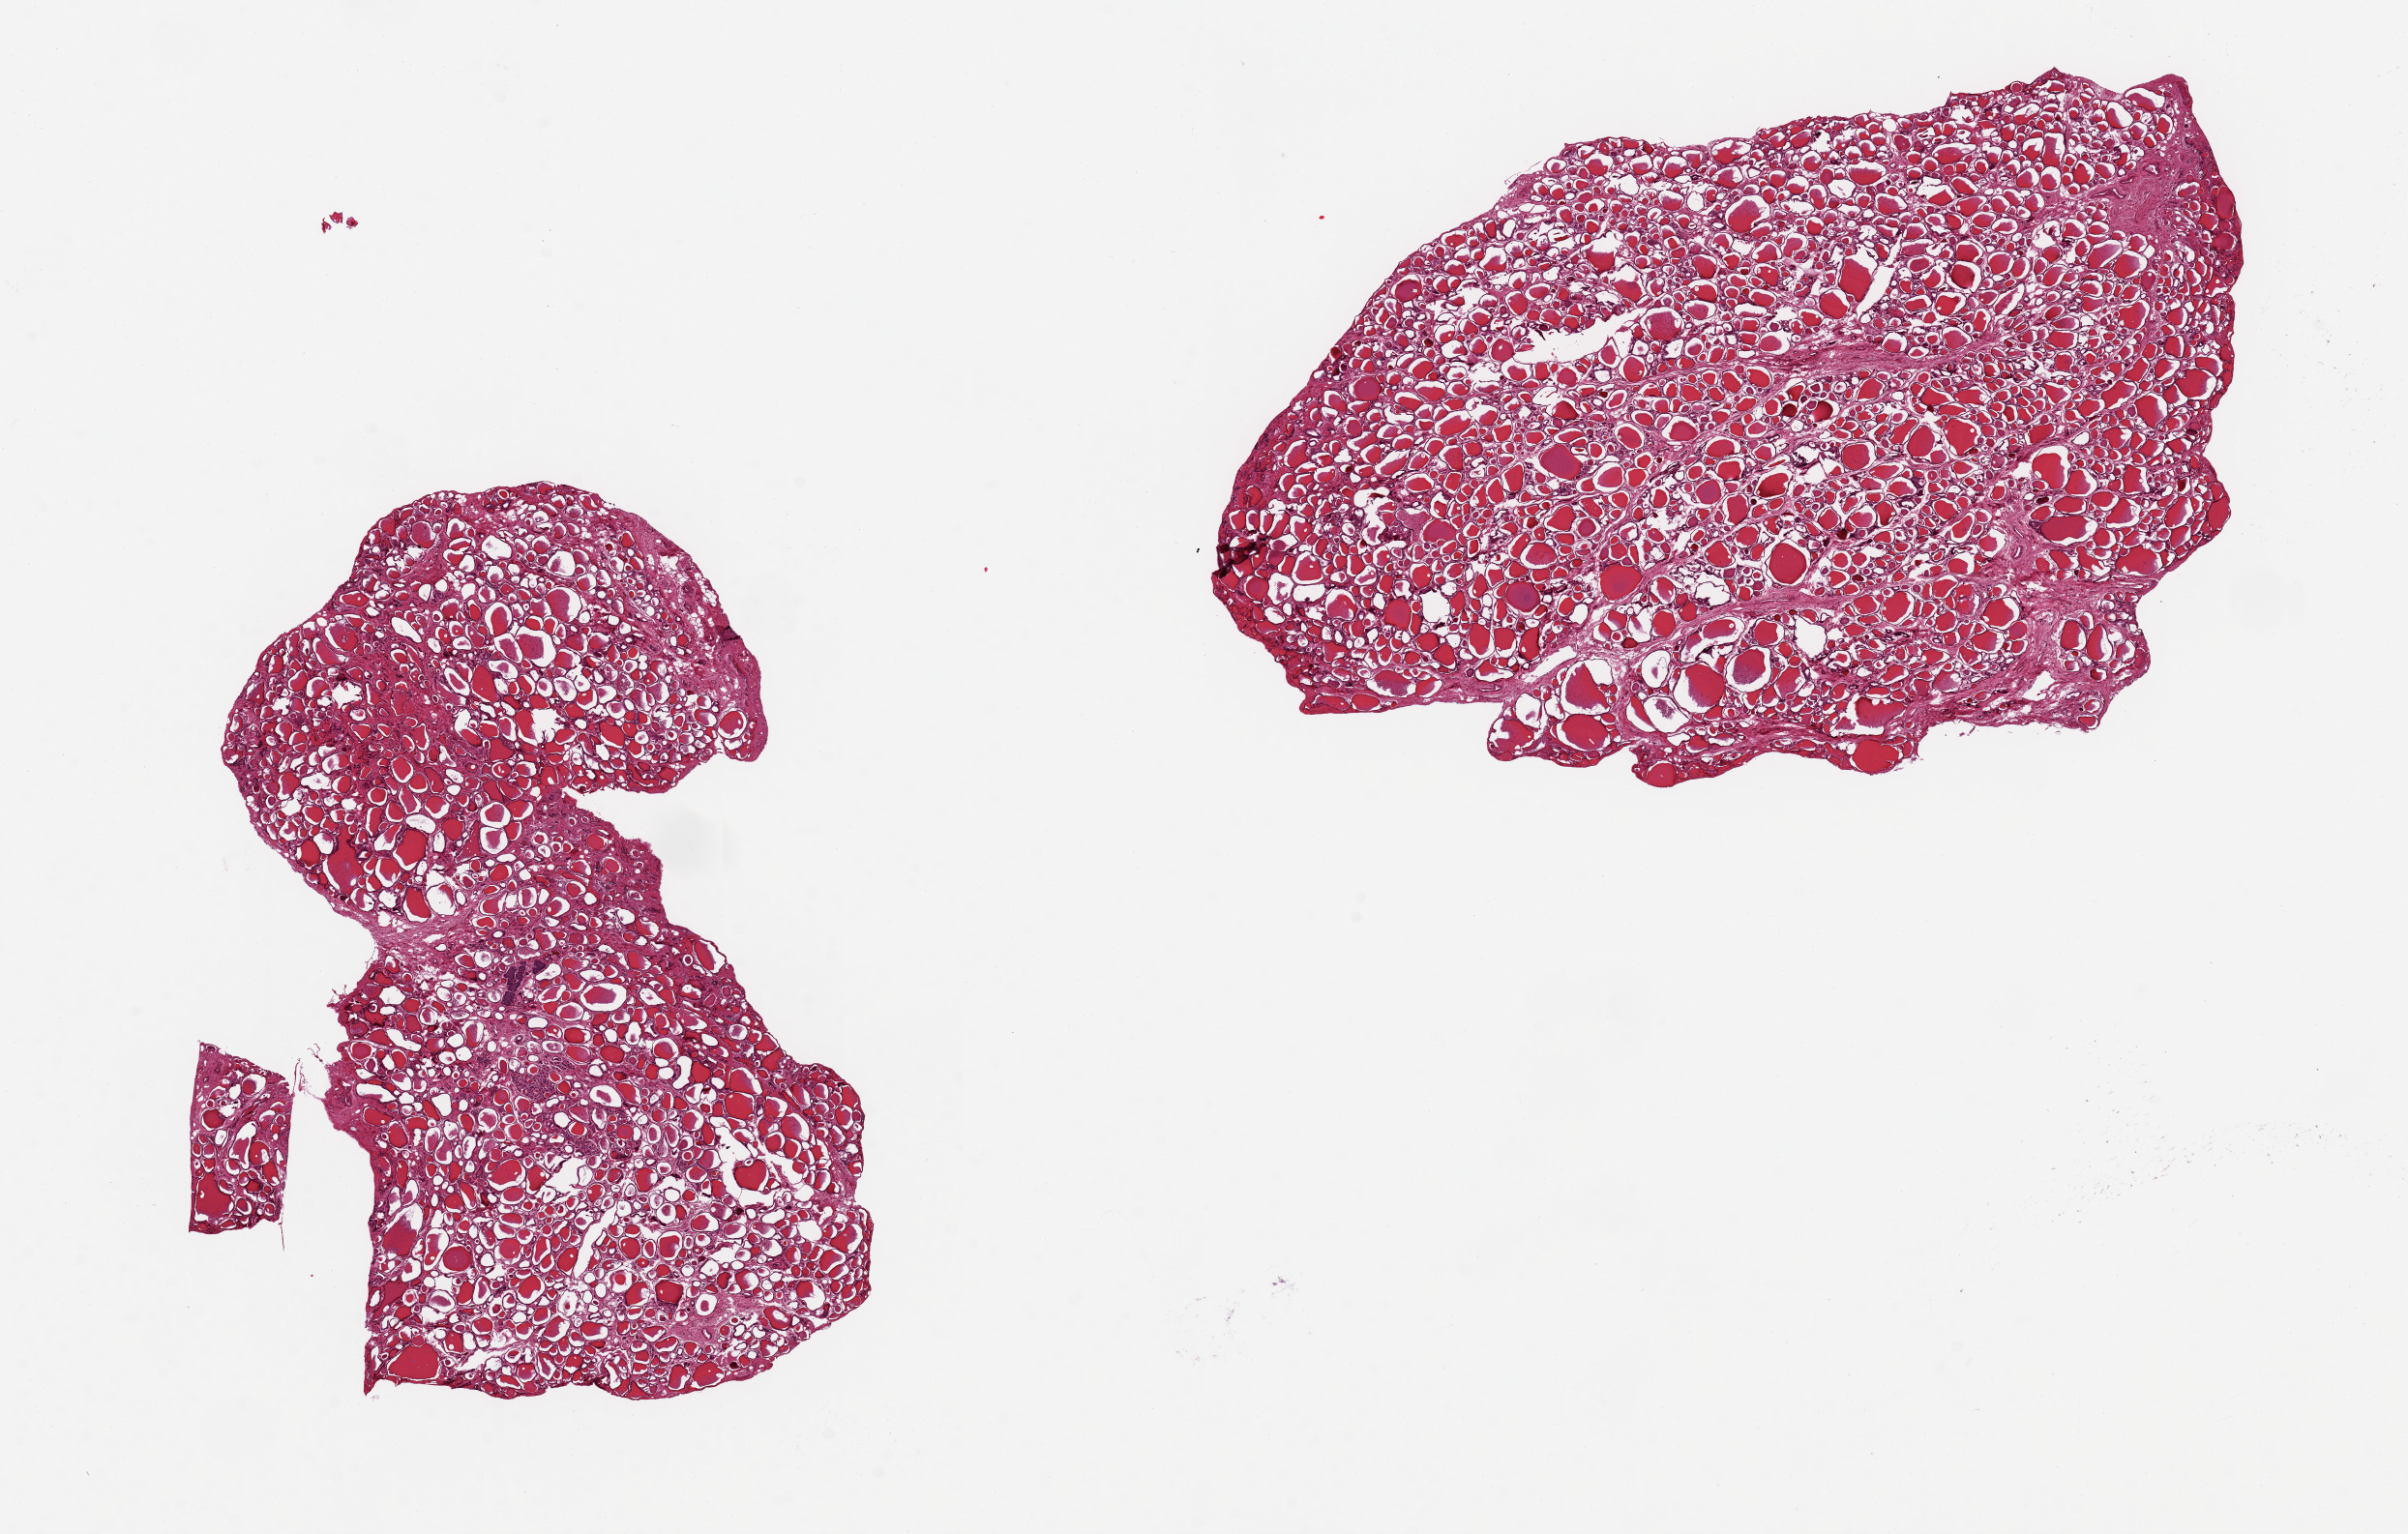
Whole-slide image, hematoxylin and eosin (H&E) stain, whole scanned area (about 19.7 x 12.5 mm, from a 20x scan) shown as a low-resolution overview. PAXgene-fixed, paraffin-embedded tissue. Section of thyroid (target tissue). Donor tissue sample. Male donor.
Review note (as recorded): 2 pieces 9x5 & 7x4 mm.